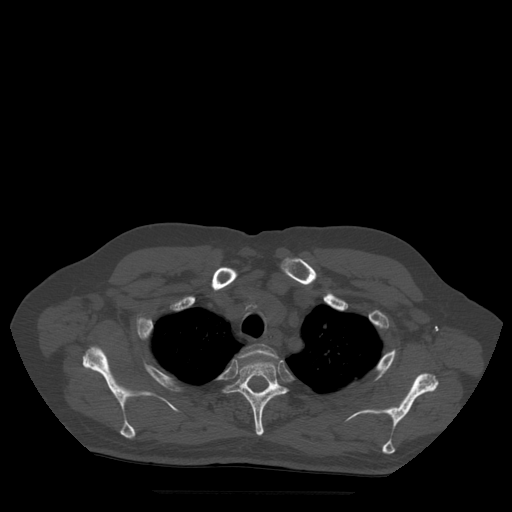
CT including the spine, one axial slice. Position 410 of 522 along the scan axis. Bone window (W 1800 / L 400 HU). 512 × 512 image matrix, field of view 420 × 420 mm. Patient age 72 years. Case-level facts recorded for this patient, not image findings: primary cancer: prostate.
Annotated regions visible in this slice (semi-automatic segmentation, software-assisted and operator-edited):
- T2 vertebra: bounding box [x1, y1, x2, y2] px = [239, 344, 278, 362]
- T3 vertebra: [224, 360, 288, 436]